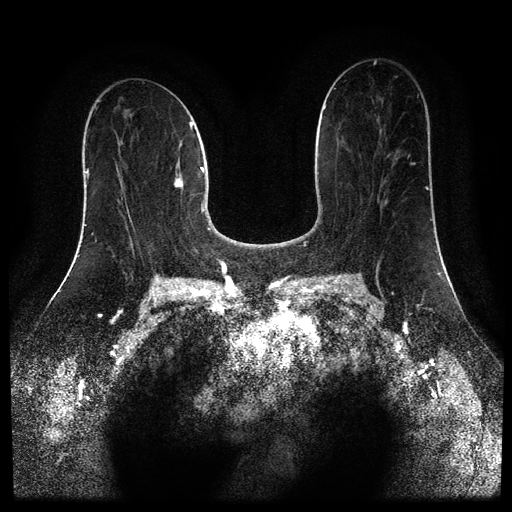
Breast MRI (dynamic contrast-enhanced, multi-phase), one axial slice; slice 45 of 110 in the series (ordered by position); dynamic contrast-enhanced series, time point 2 of 5 at this slice position (early post-contrast); 1.5 T; TE 2.6 ms, TR 5.4 ms; 512 × 512 image matrix, field of view 340 × 340 mm. Female patient, age 43 years.
Annotated regions visible in this slice (semi-automatically segmented with operator editing):
- breast lesion (labelled 'tumour' in the annotation; benign lesions carry a separate 'benign' label): bounding box <174,174,184,189> (left, top, right, bottom; pixels)